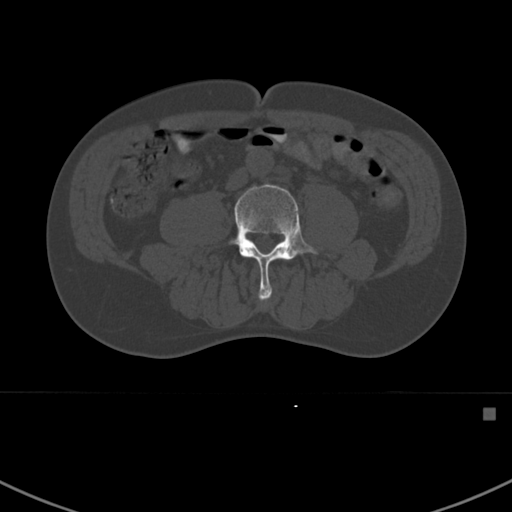
CT including the spine, one axial slice. Slice 242 of 412 in the series (ordered by position). Reconstruction kernel Br40s. 120 kVp. Bone window (W 1800 / L 400 HU). 1.5 mm slice thickness. 512 × 512 image matrix. Patient: male, 59 years. From the clinical record (not read from this slice): primary cancer: prostate.
Annotated regions visible in this slice (semi-automatic segmentation, software-assisted and operator-edited):
- L3 vertebra: bounding box [x1, y1, x2, y2] px = [266, 297, 269, 299]
- L4 vertebra: [229, 184, 318, 301]